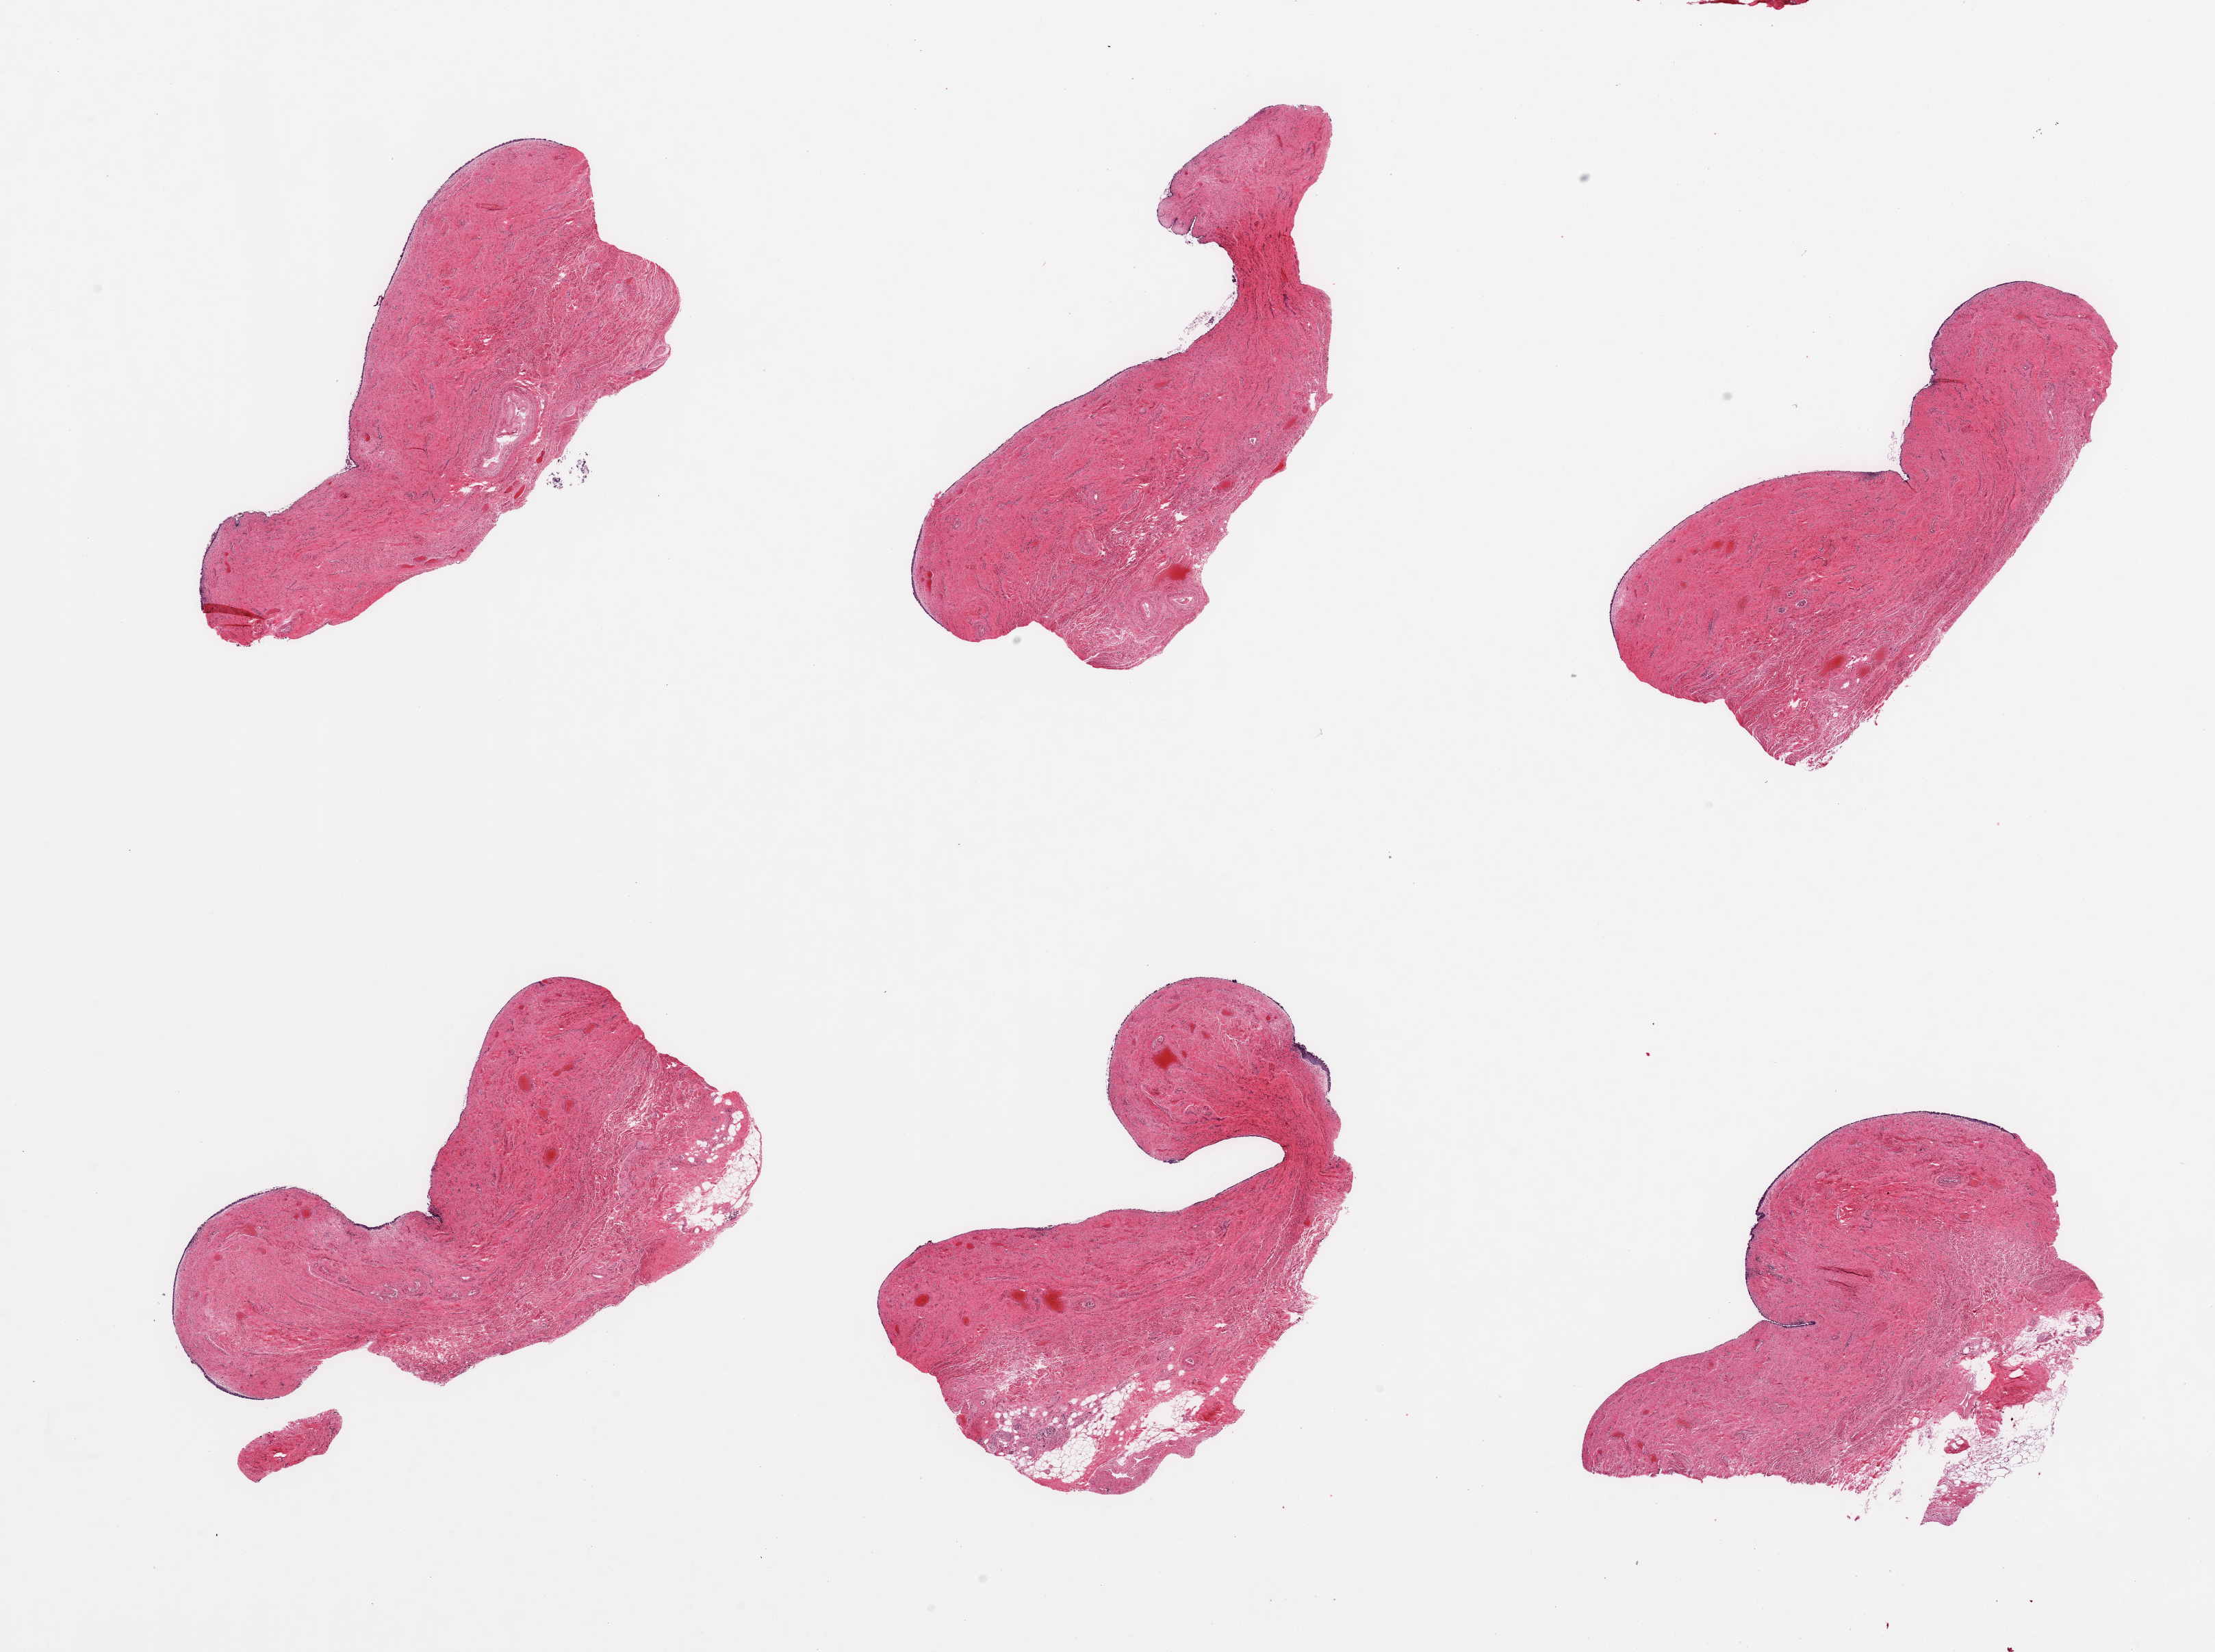
Whole-slide image, haematoxylin and eosin stain — whole scanned area (about 25.6 x 19.1 mm) shown as a low-resolution overview. PAXgene-fixed paraffin-embedded (PFPE) section. Sampled site (target tissue): vagina. Tissue donor sample. Donor sex: female.
Review note (as recorded): 6 pieces; epithelium is atrophic/partially sloughed.